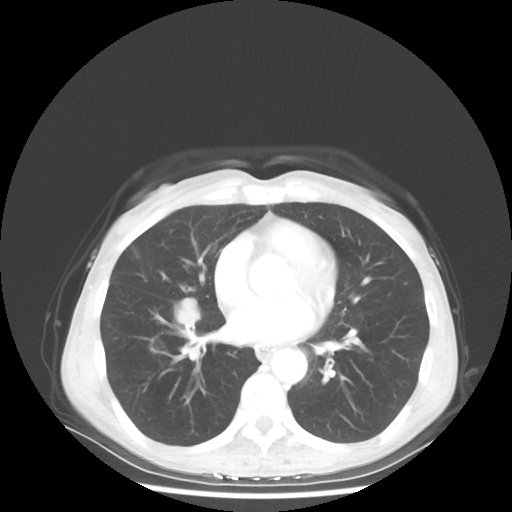
Chest CT, one axial slice. Position 24 of 56 along the scan axis. Lung window (W 1500 / L -600 HU). 5 mm slice thickness. 512 × 512 image matrix. Patient: female, 57 years. Case-level facts recorded for this patient, not image findings: clinical TNM (as recorded): T1c N3 M1a.
Annotated regions visible in this slice (rectangle marked by the reading radiologist):
- lung tumour (recorded histology: adenocarcinoma): box from (x=175, y=291) to (x=203, y=330) px